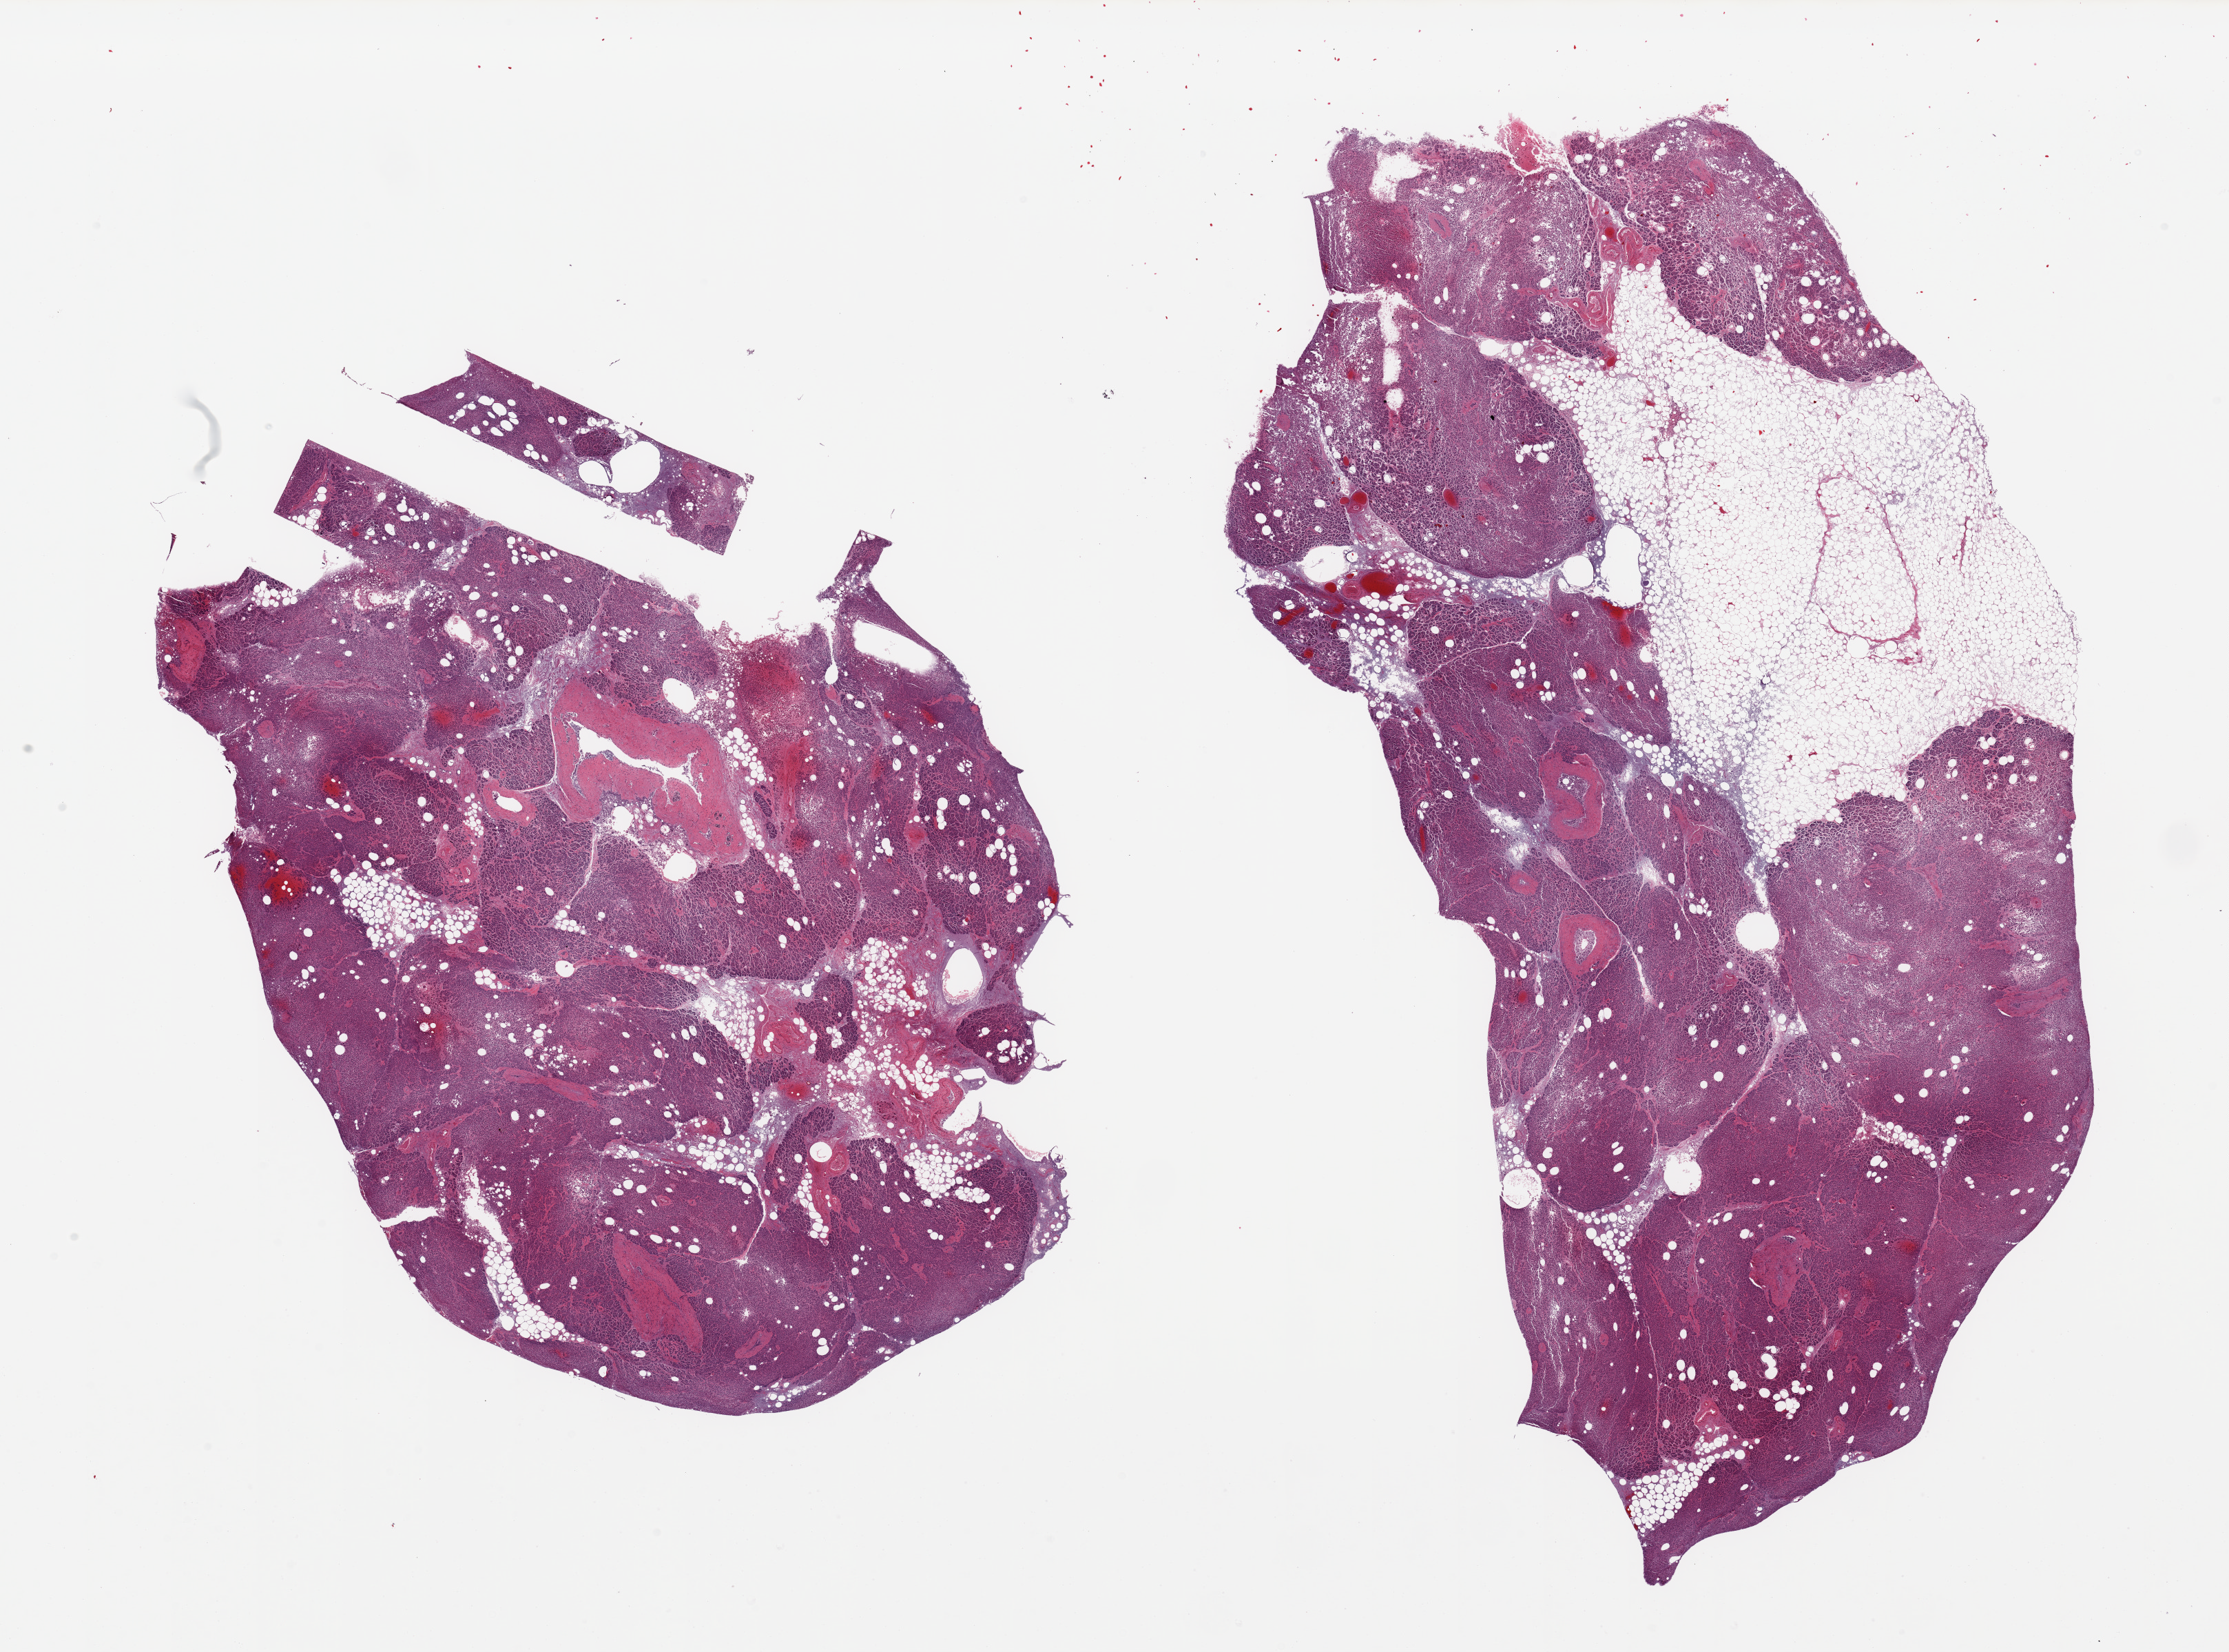
Haematoxylin and eosin whole-slide image, brightfield, shown as a low-resolution overview of the whole scanned area (about 25.6 x 19.0 mm, acquisition: 20x scan), PAXgene-fixed, paraffin-embedded tissue, target tissue: pancreas, donor tissue sample. Donor: female.
Reviewer comment on this tissue sample: 2 pieces, moderate-advanced saponification, ~15% adherent fat; Islets not well preserved.